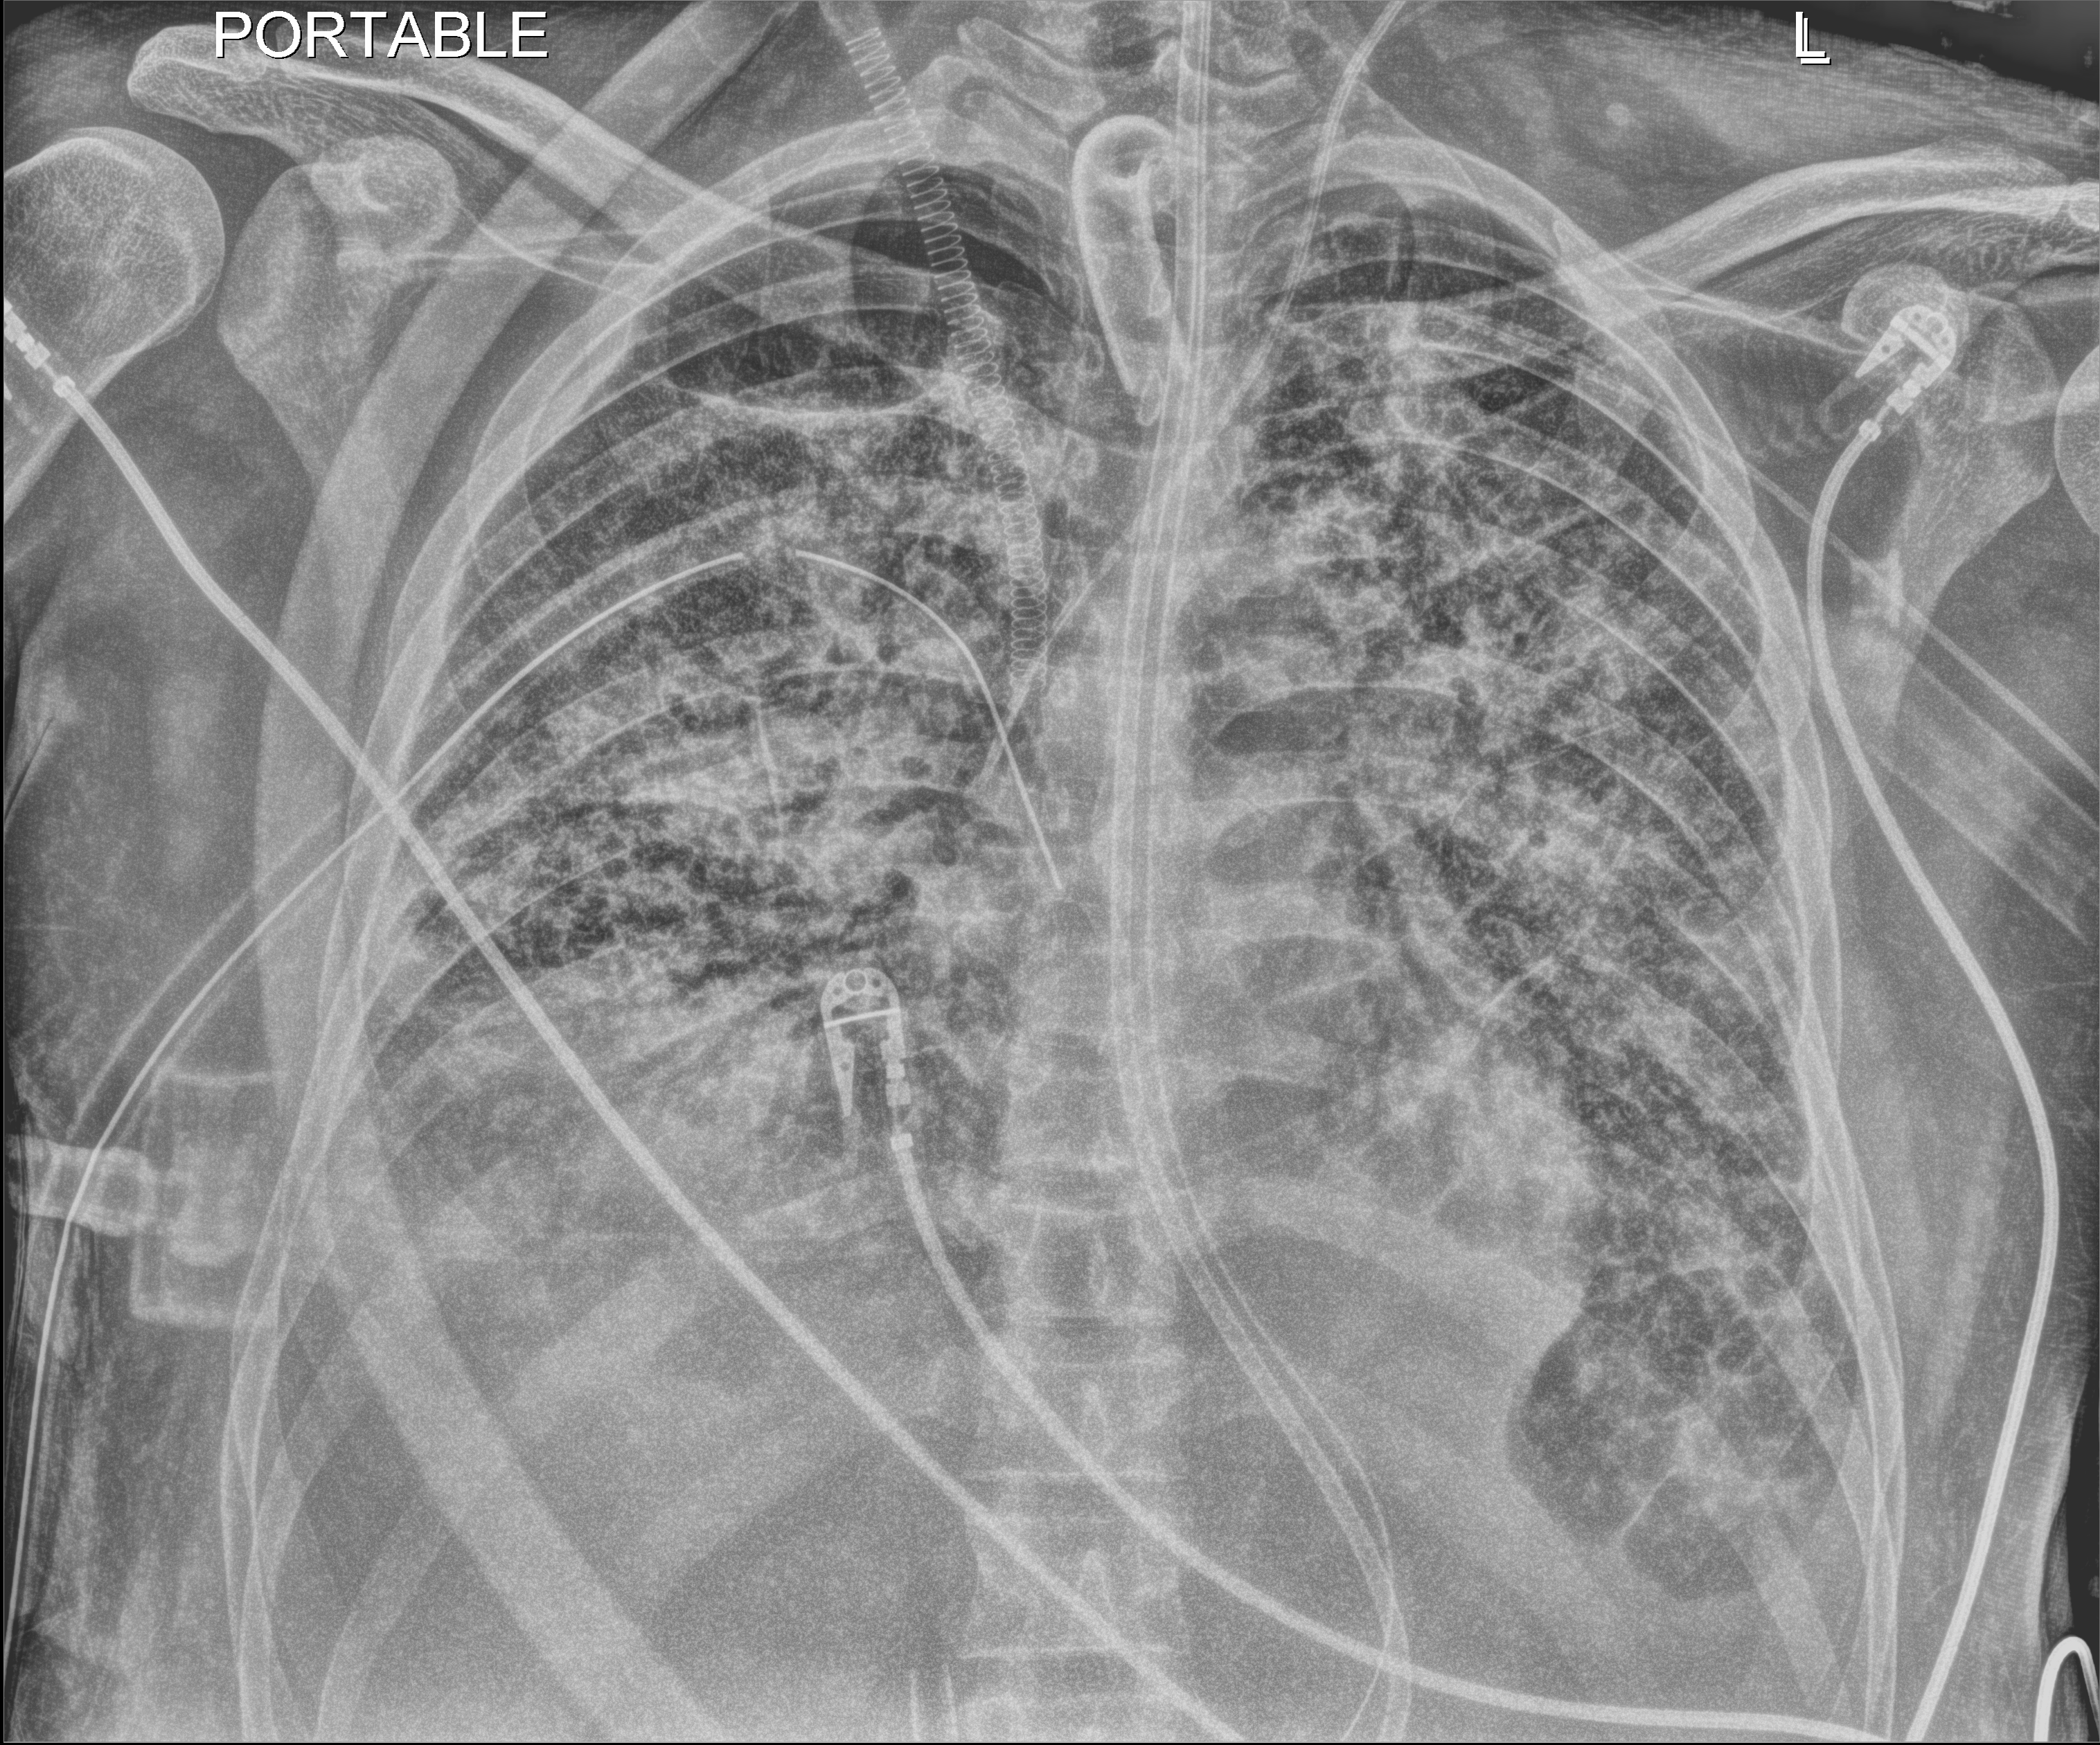
Portable chest radiograph. Patient hospitalised with COVID-19, aged 18–59 years.
From the hospital-stay record, not from the radiograph (when in the stay this image was taken is not recorded): length of hospital stay: 60 days; smoking status (admission record): never; admitted to intensive care during this hospital stay: yes.